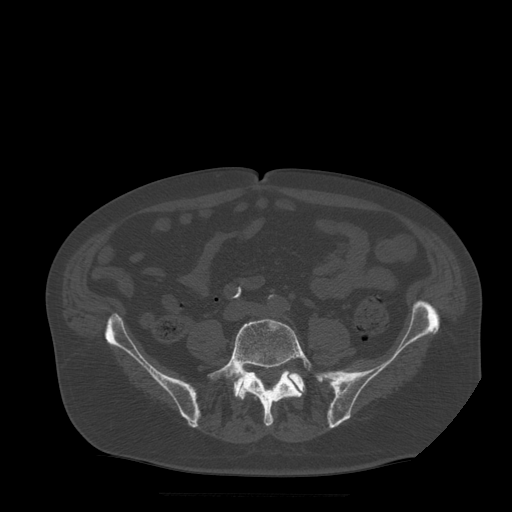
CT including the spine, one axial slice. Position 87 of 522 along the scan axis. Bone window (W 1800 / L 400 HU). 1.25 mm slice thickness. 512 × 512 image matrix, field of view 420 × 420 mm. Patient age 72 years. From the clinical record (not read from this slice): primary cancer: prostate.
Outlined on this slice (semi-automatically segmented with operator editing):
- L5 vertebra: bounding box [x1, y1, x2, y2] px = [208, 319, 331, 427]